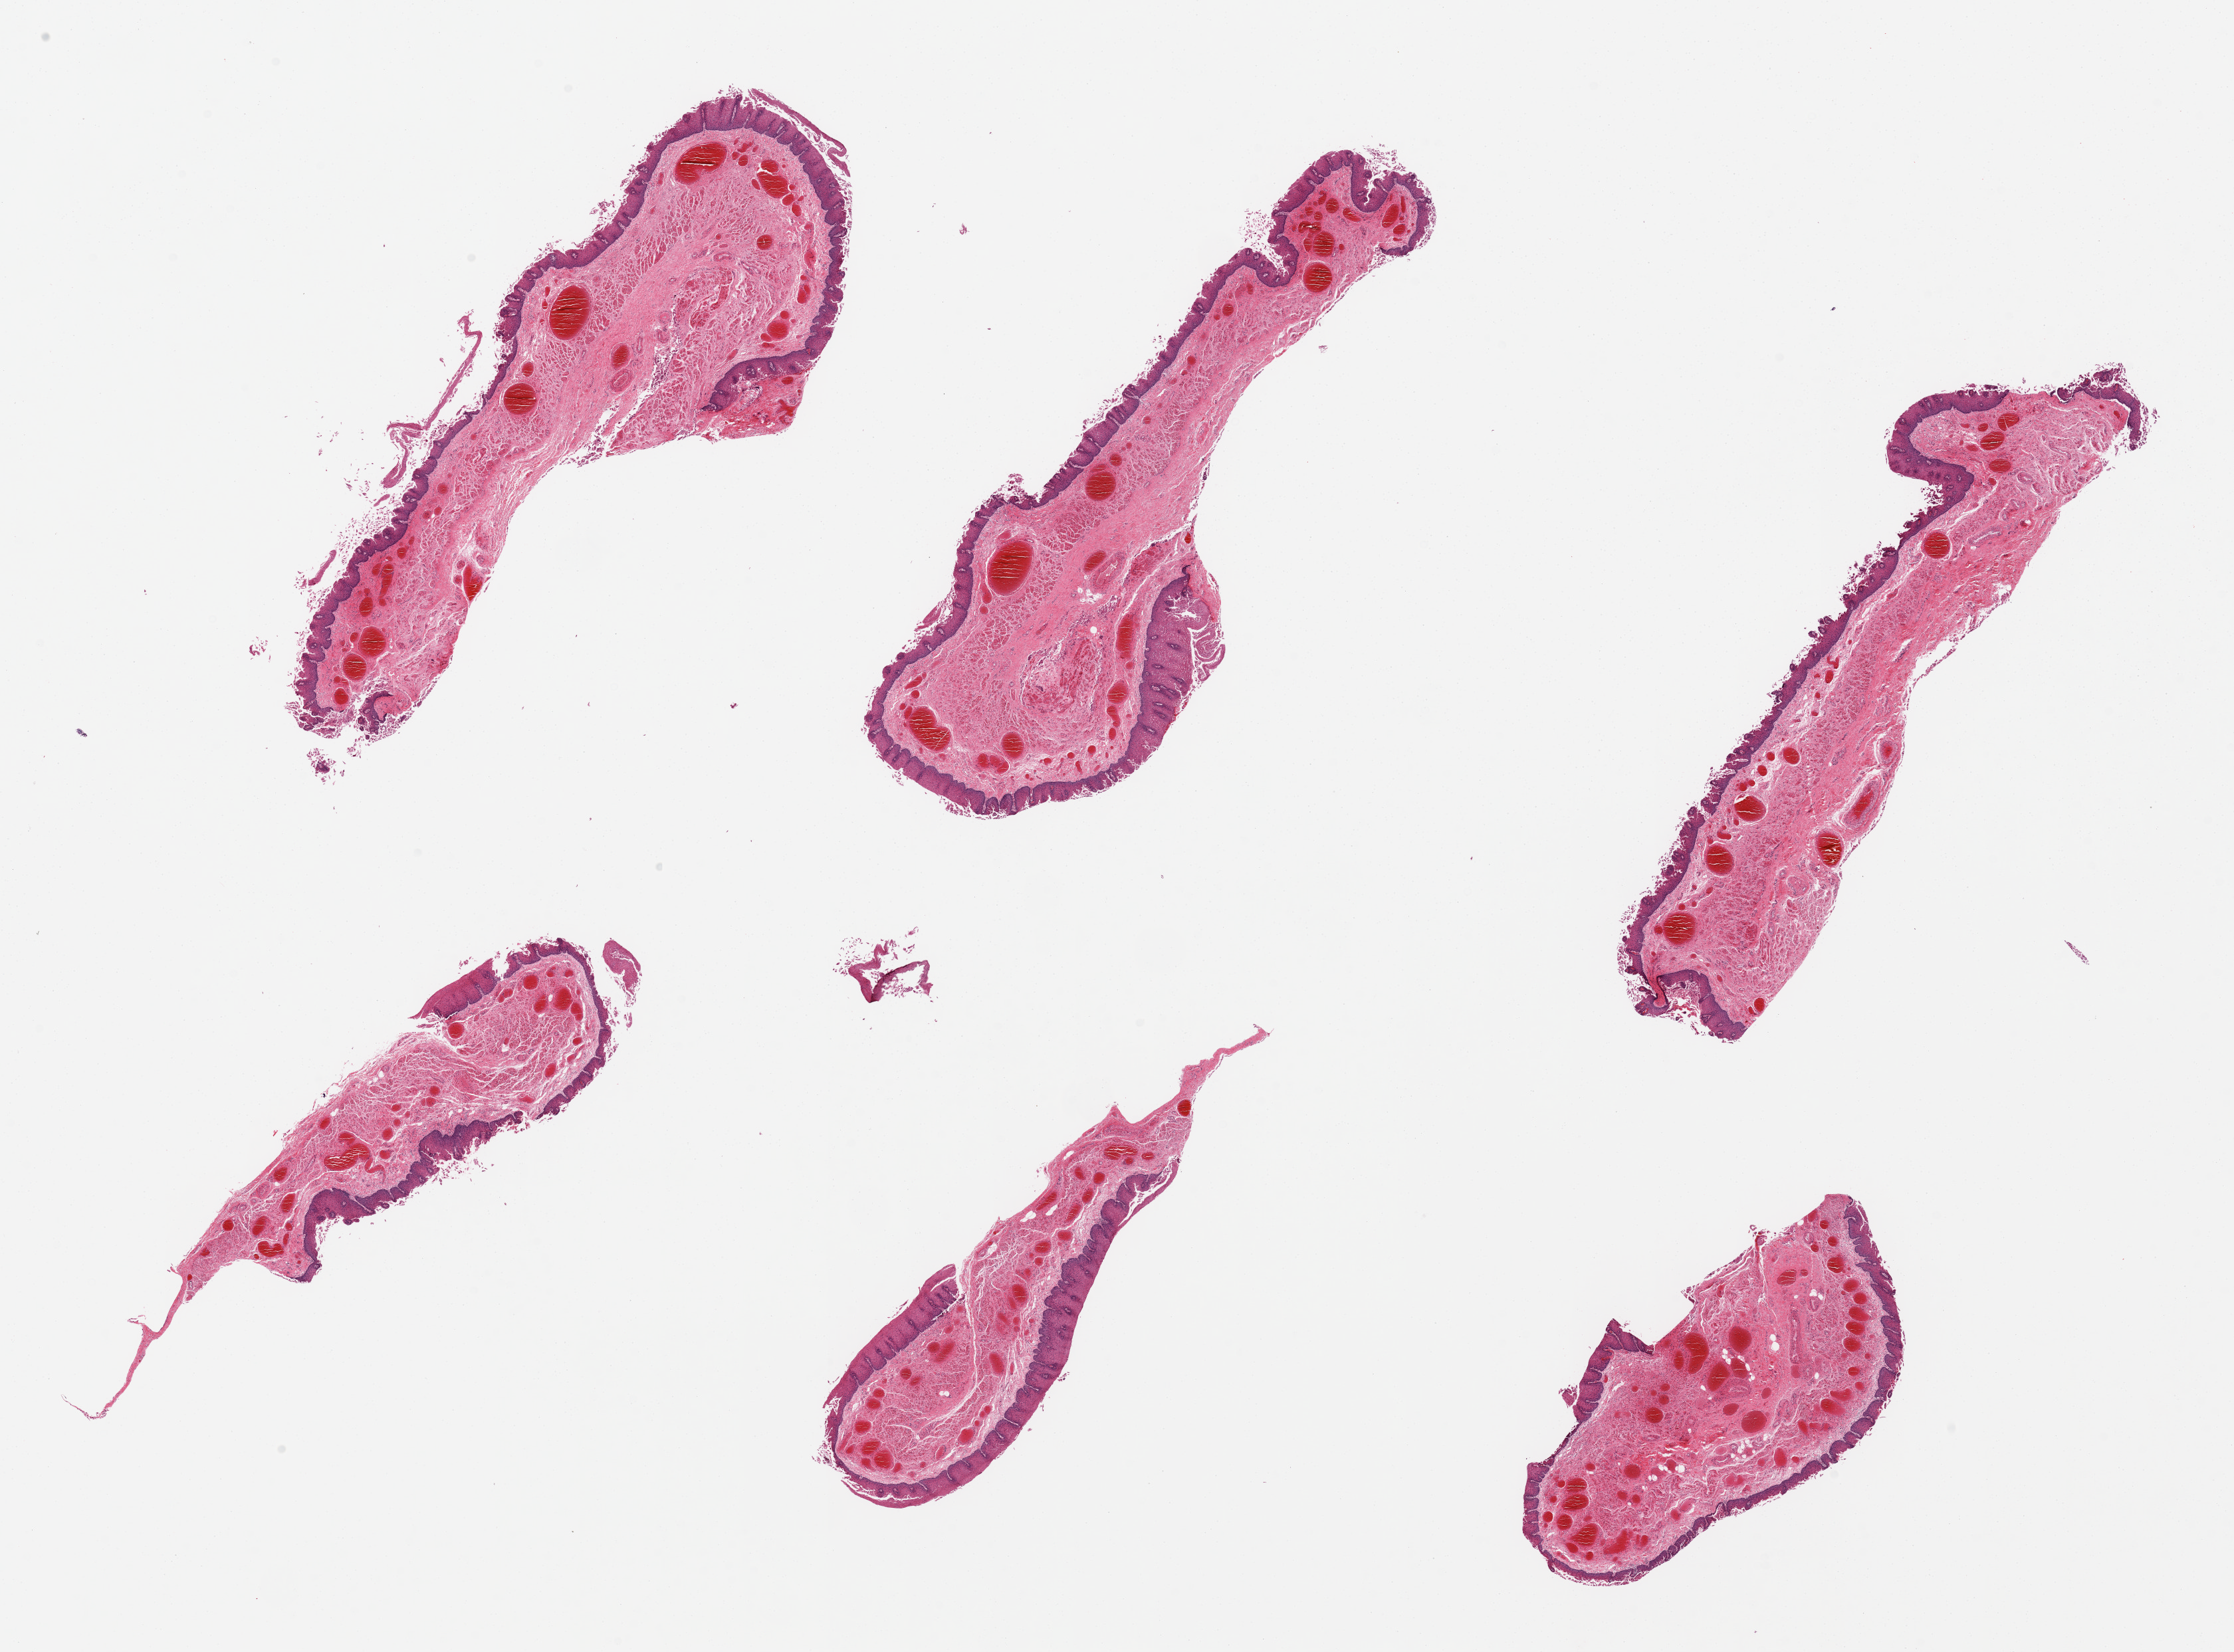
Digitized H&E-stained section, shown as a low-resolution overview of the whole scanned area (about 26.6 x 19.7 mm, slide scanned at 20x), PAXgene-fixed, paraffin-embedded tissue, target tissue: esophageal mucous membrane, donor tissue sample.
Pathologist's review note for this sample: 6 pieces, congestion.